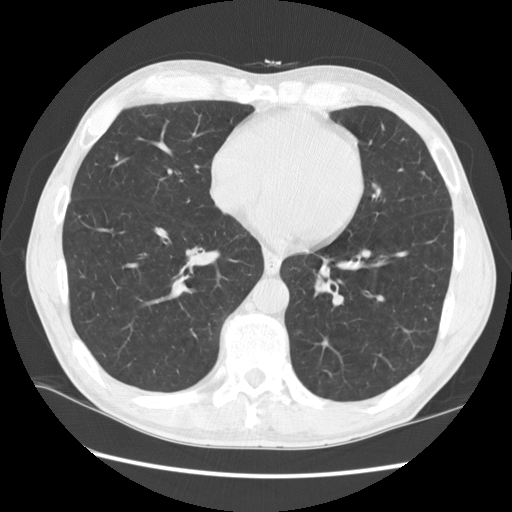
Low-dose screening chest CT, one axial slice. Position 50 of 141 along the scan axis. Lung window (W 1500 / L -600 HU). 2.5 mm slice thickness. 512 × 512 image matrix, field of view 360 × 360 mm.
Structures marked on this image (outlined manually by an expert reader):
- lesion 2 (nodule, lower lobe of left lung): bounding box <314,277,330,297> (left, top, right, bottom; pixels)